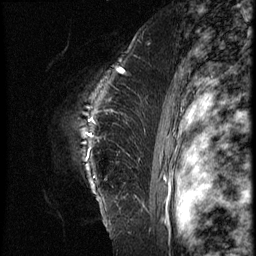
Breast MRI (dynamic contrast-enhanced), one sagittal slice; position 50 of 62 along the scan axis; 3 images stored at this slice position (order not interpretable as contrast timing); 1.5 T; TE 4.2 ms, TR 9 ms; 2.5 mm slice thickness; 256 × 256 image matrix. Patient: female, 39 years. From the clinical record (not read from this slice): setting: breast cancer imaged before/during neoadjuvant chemotherapy; receptor status: HER2-positive.
Structures marked on this image (semi-automatically segmented with operator editing):
- analysis volume of interest (the breast-tissue region the enhancement analysis was run in; not a lesion): bounding box (x1, y1, x2, y2) in pixels: (45, 64, 152, 228)
- tumour enhancement mask (voxels above the 140 % enhancement threshold inside the analysis volume of interest): (93, 68, 126, 120)